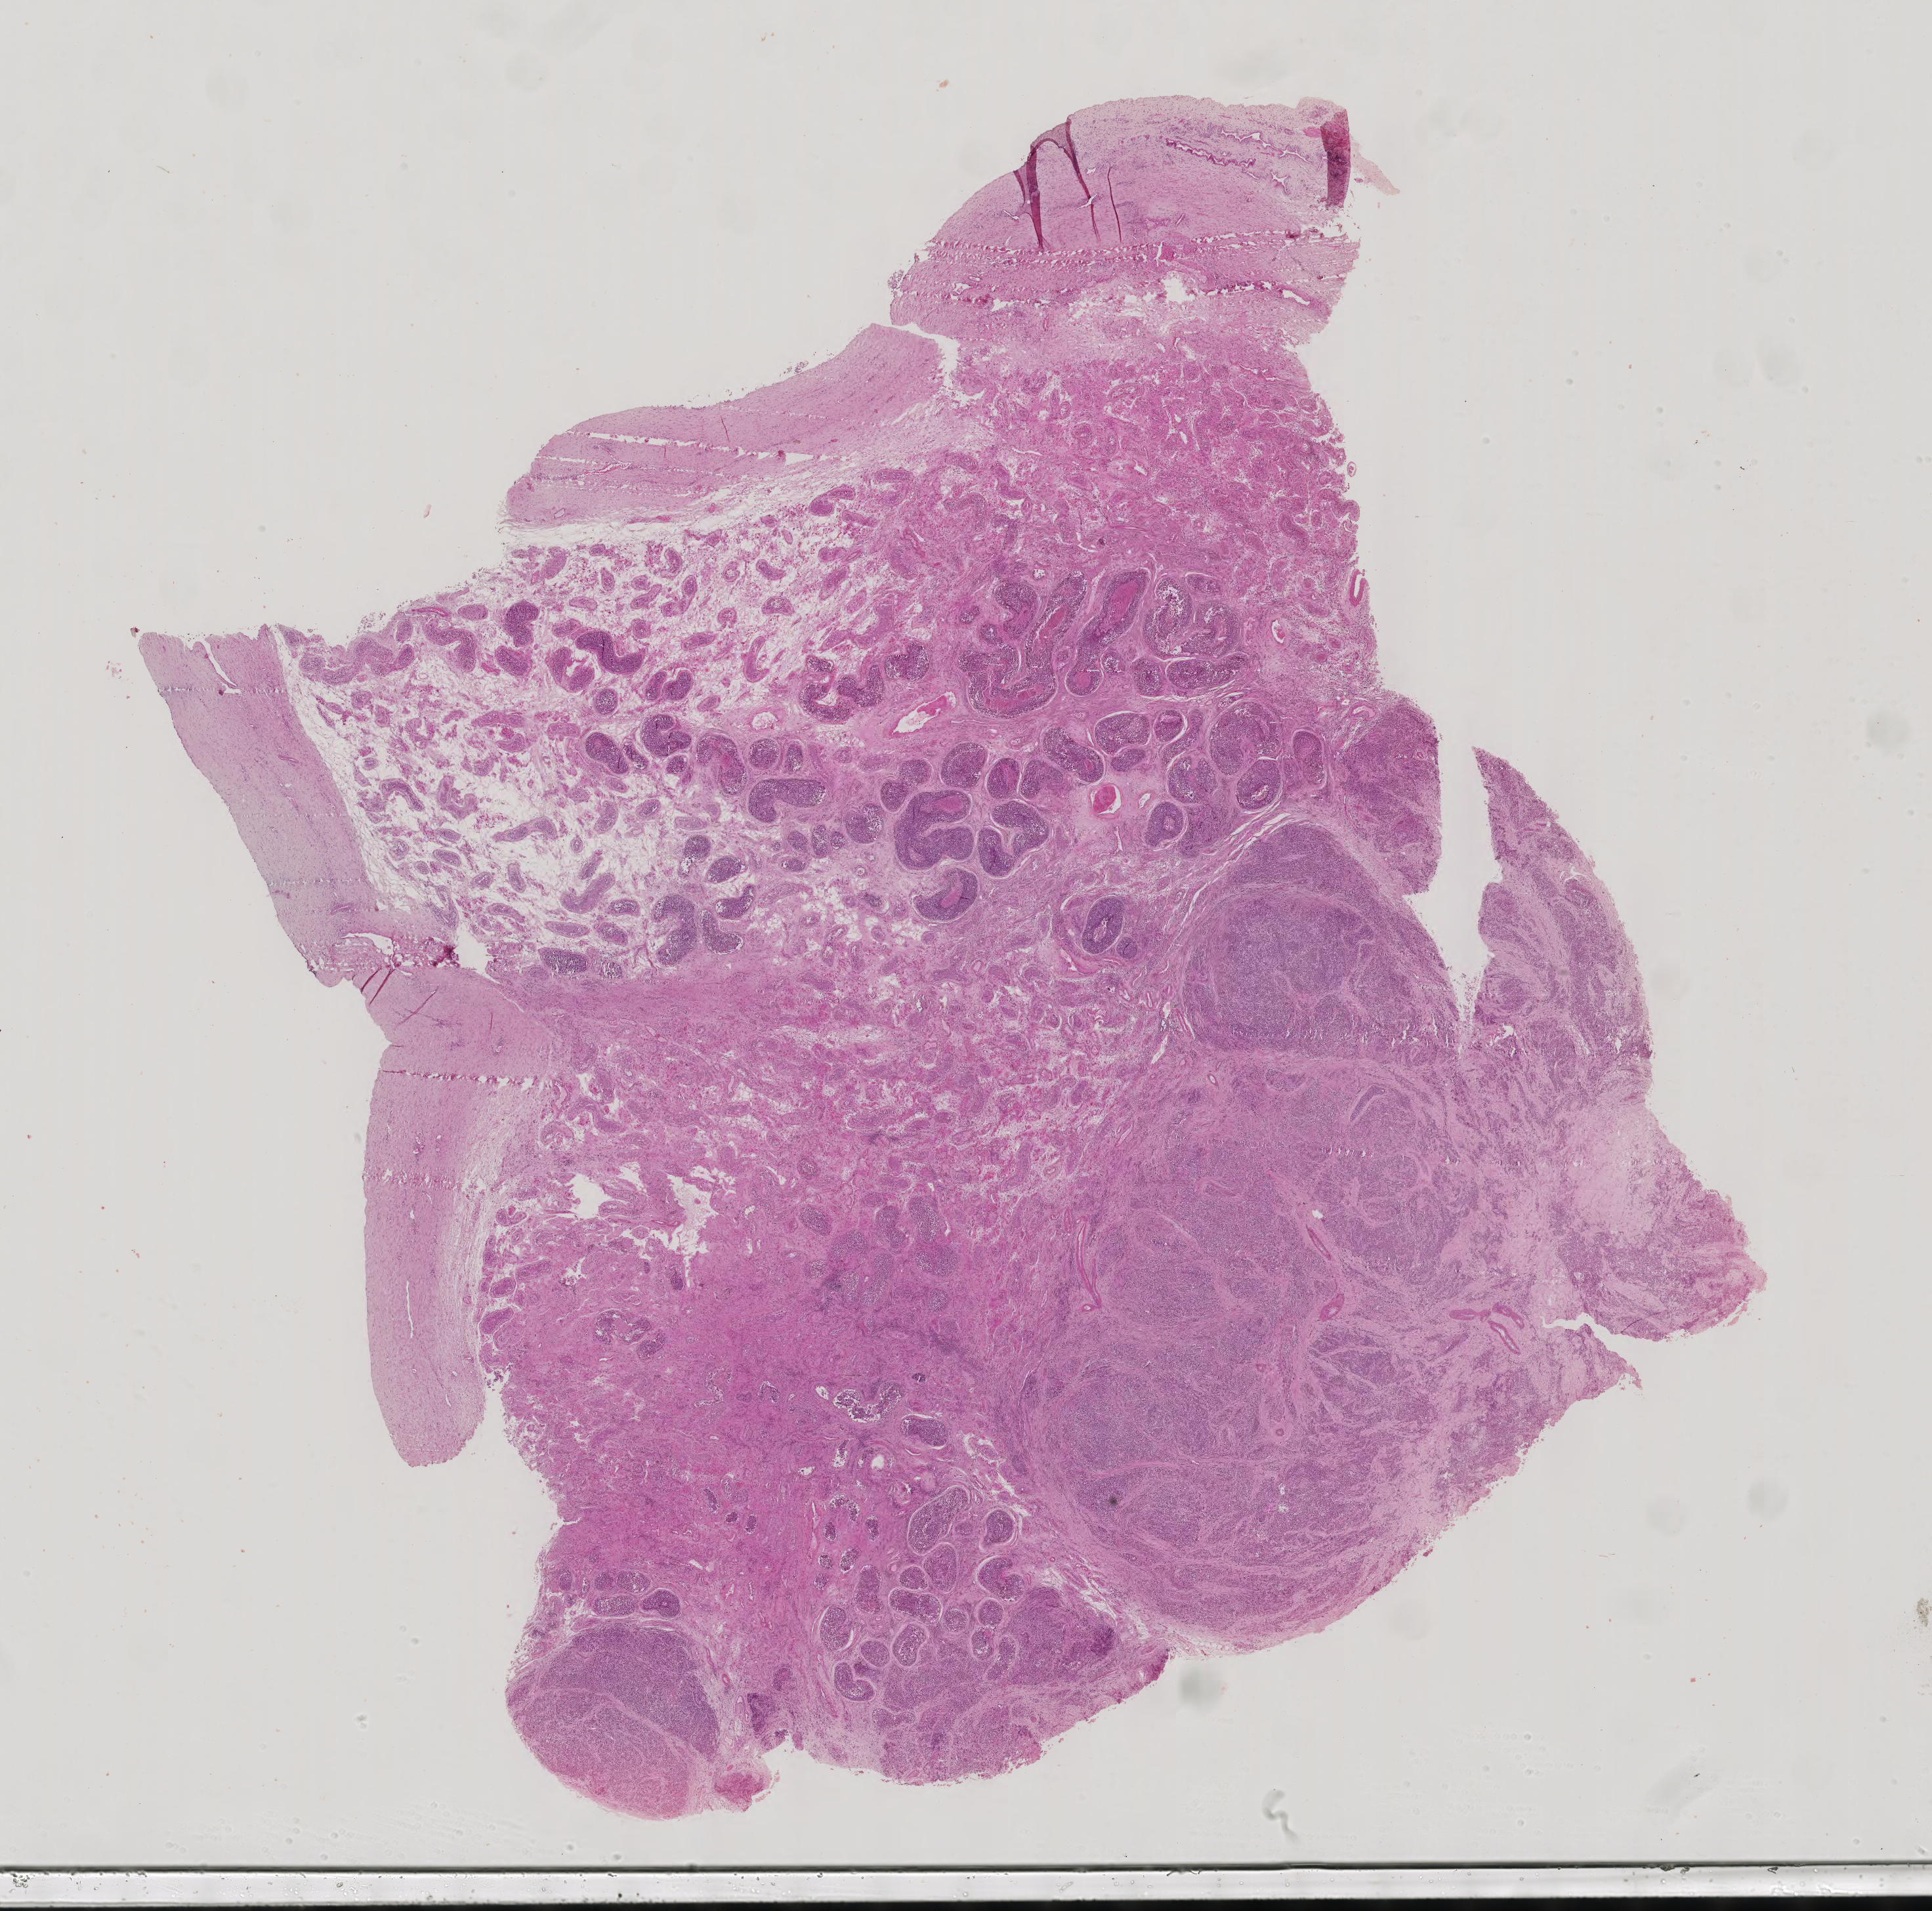
H&E whole-slide image — shown as a low-resolution overview of the whole scanned area (about 21.5 x 21.2 mm, slide scanned at 40x), formalin-fixed paraffin-embedded (FFPE) diagnostic section, sample: primary tumour, testis. Patient: male, age at initial diagnosis 20 years.
Laterality: right. TNM: T2 NX M0. AJCC pathologic stage: I. Histologic diagnosis: Seminoma, NOS.